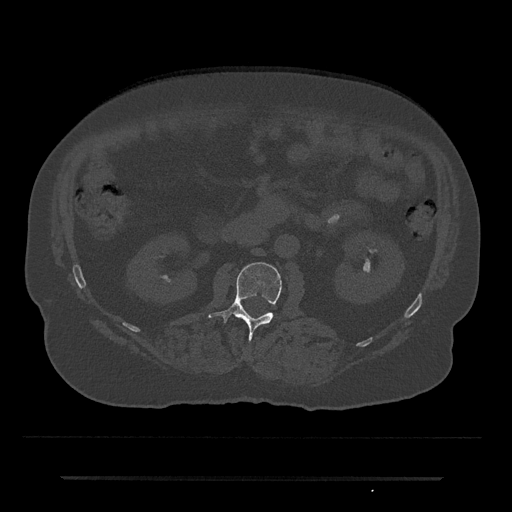
CT including the spine, one axial slice. Slice 10 of 797 in the series (ordered by position). Reconstruction kernel Br40s/3. 120 kVp. Bone window (W 1800 / L 400 HU). 0.5 mm slice thickness. 512 × 512 image matrix, field of view 437 × 437 mm. Patient: male, 69 years. From the clinical record (not read from this slice): primary cancer: prostate.
Outlined on this slice (semi-automatically segmented with operator editing):
- L2 vertebra: bounding box [x1, y1, x2, y2] px = [208, 262, 282, 340]